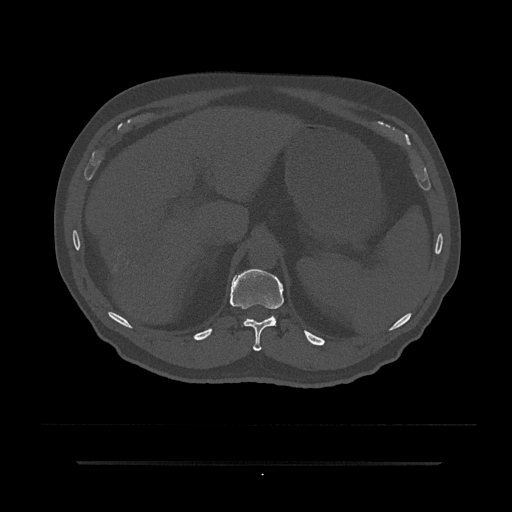
CT including the spine, one axial slice. Position 255 of 797 along the scan axis. Reconstruction kernel Br40s/3. 120 kVp. Bone window (W 1800 / L 400 HU). 0.5 mm slice thickness. 512 × 512 image matrix, field of view 464 × 464 mm. Patient: male, 59 years. From the clinical record (not read from this slice): primary cancer: bile ducts; vertebrae with lytic lesions (as recorded): T10.
Structures marked on this image (semi-automatically segmented with operator editing):
- T11 vertebra: bounding box (x1, y1, x2, y2) in pixels: (230, 269, 284, 351)
- T12 vertebra: (244, 316, 276, 322)